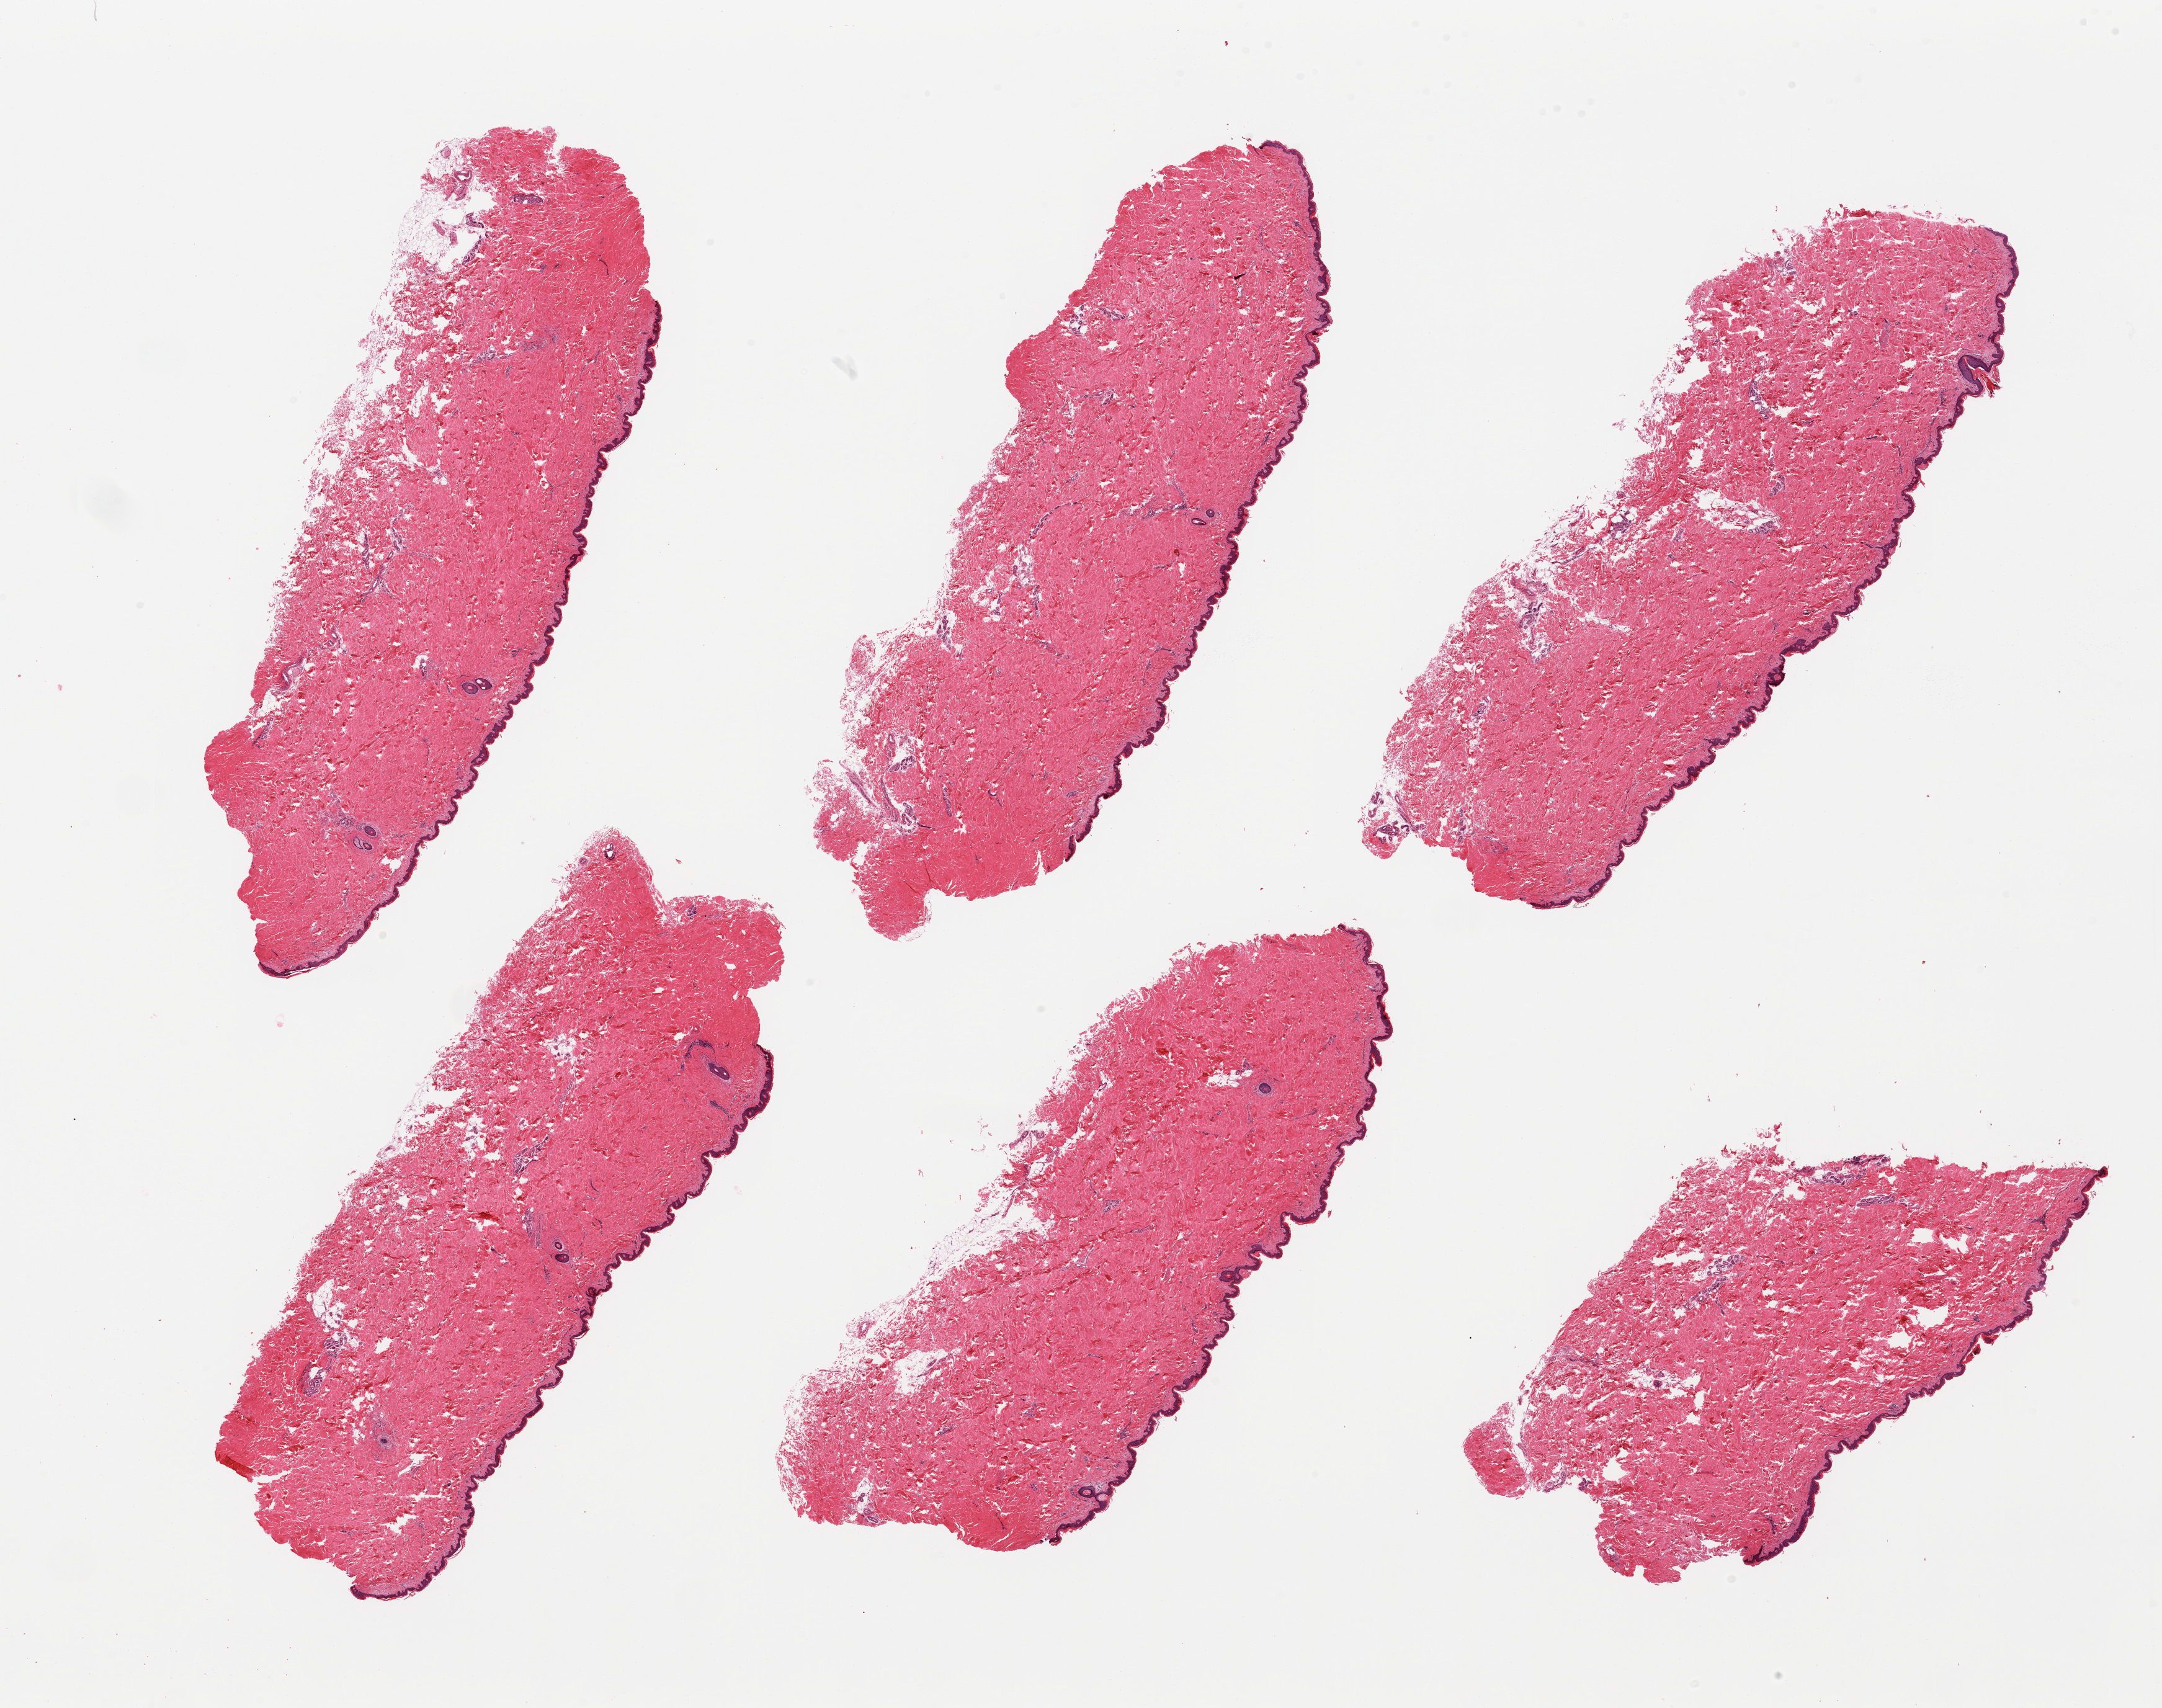
H&E whole-slide image, brightfield — low-resolution overview of the scanned area, about 27.6 x 21.8 mm, PAXgene-fixed paraffin-embedded (PFPE) section, sampled site (target tissue): skin of suprapubic region, tissue donor sample. Donor sex: male.
Pathologist's review note for this sample: 6 pieces; well trimmed; 2% dermal fat.